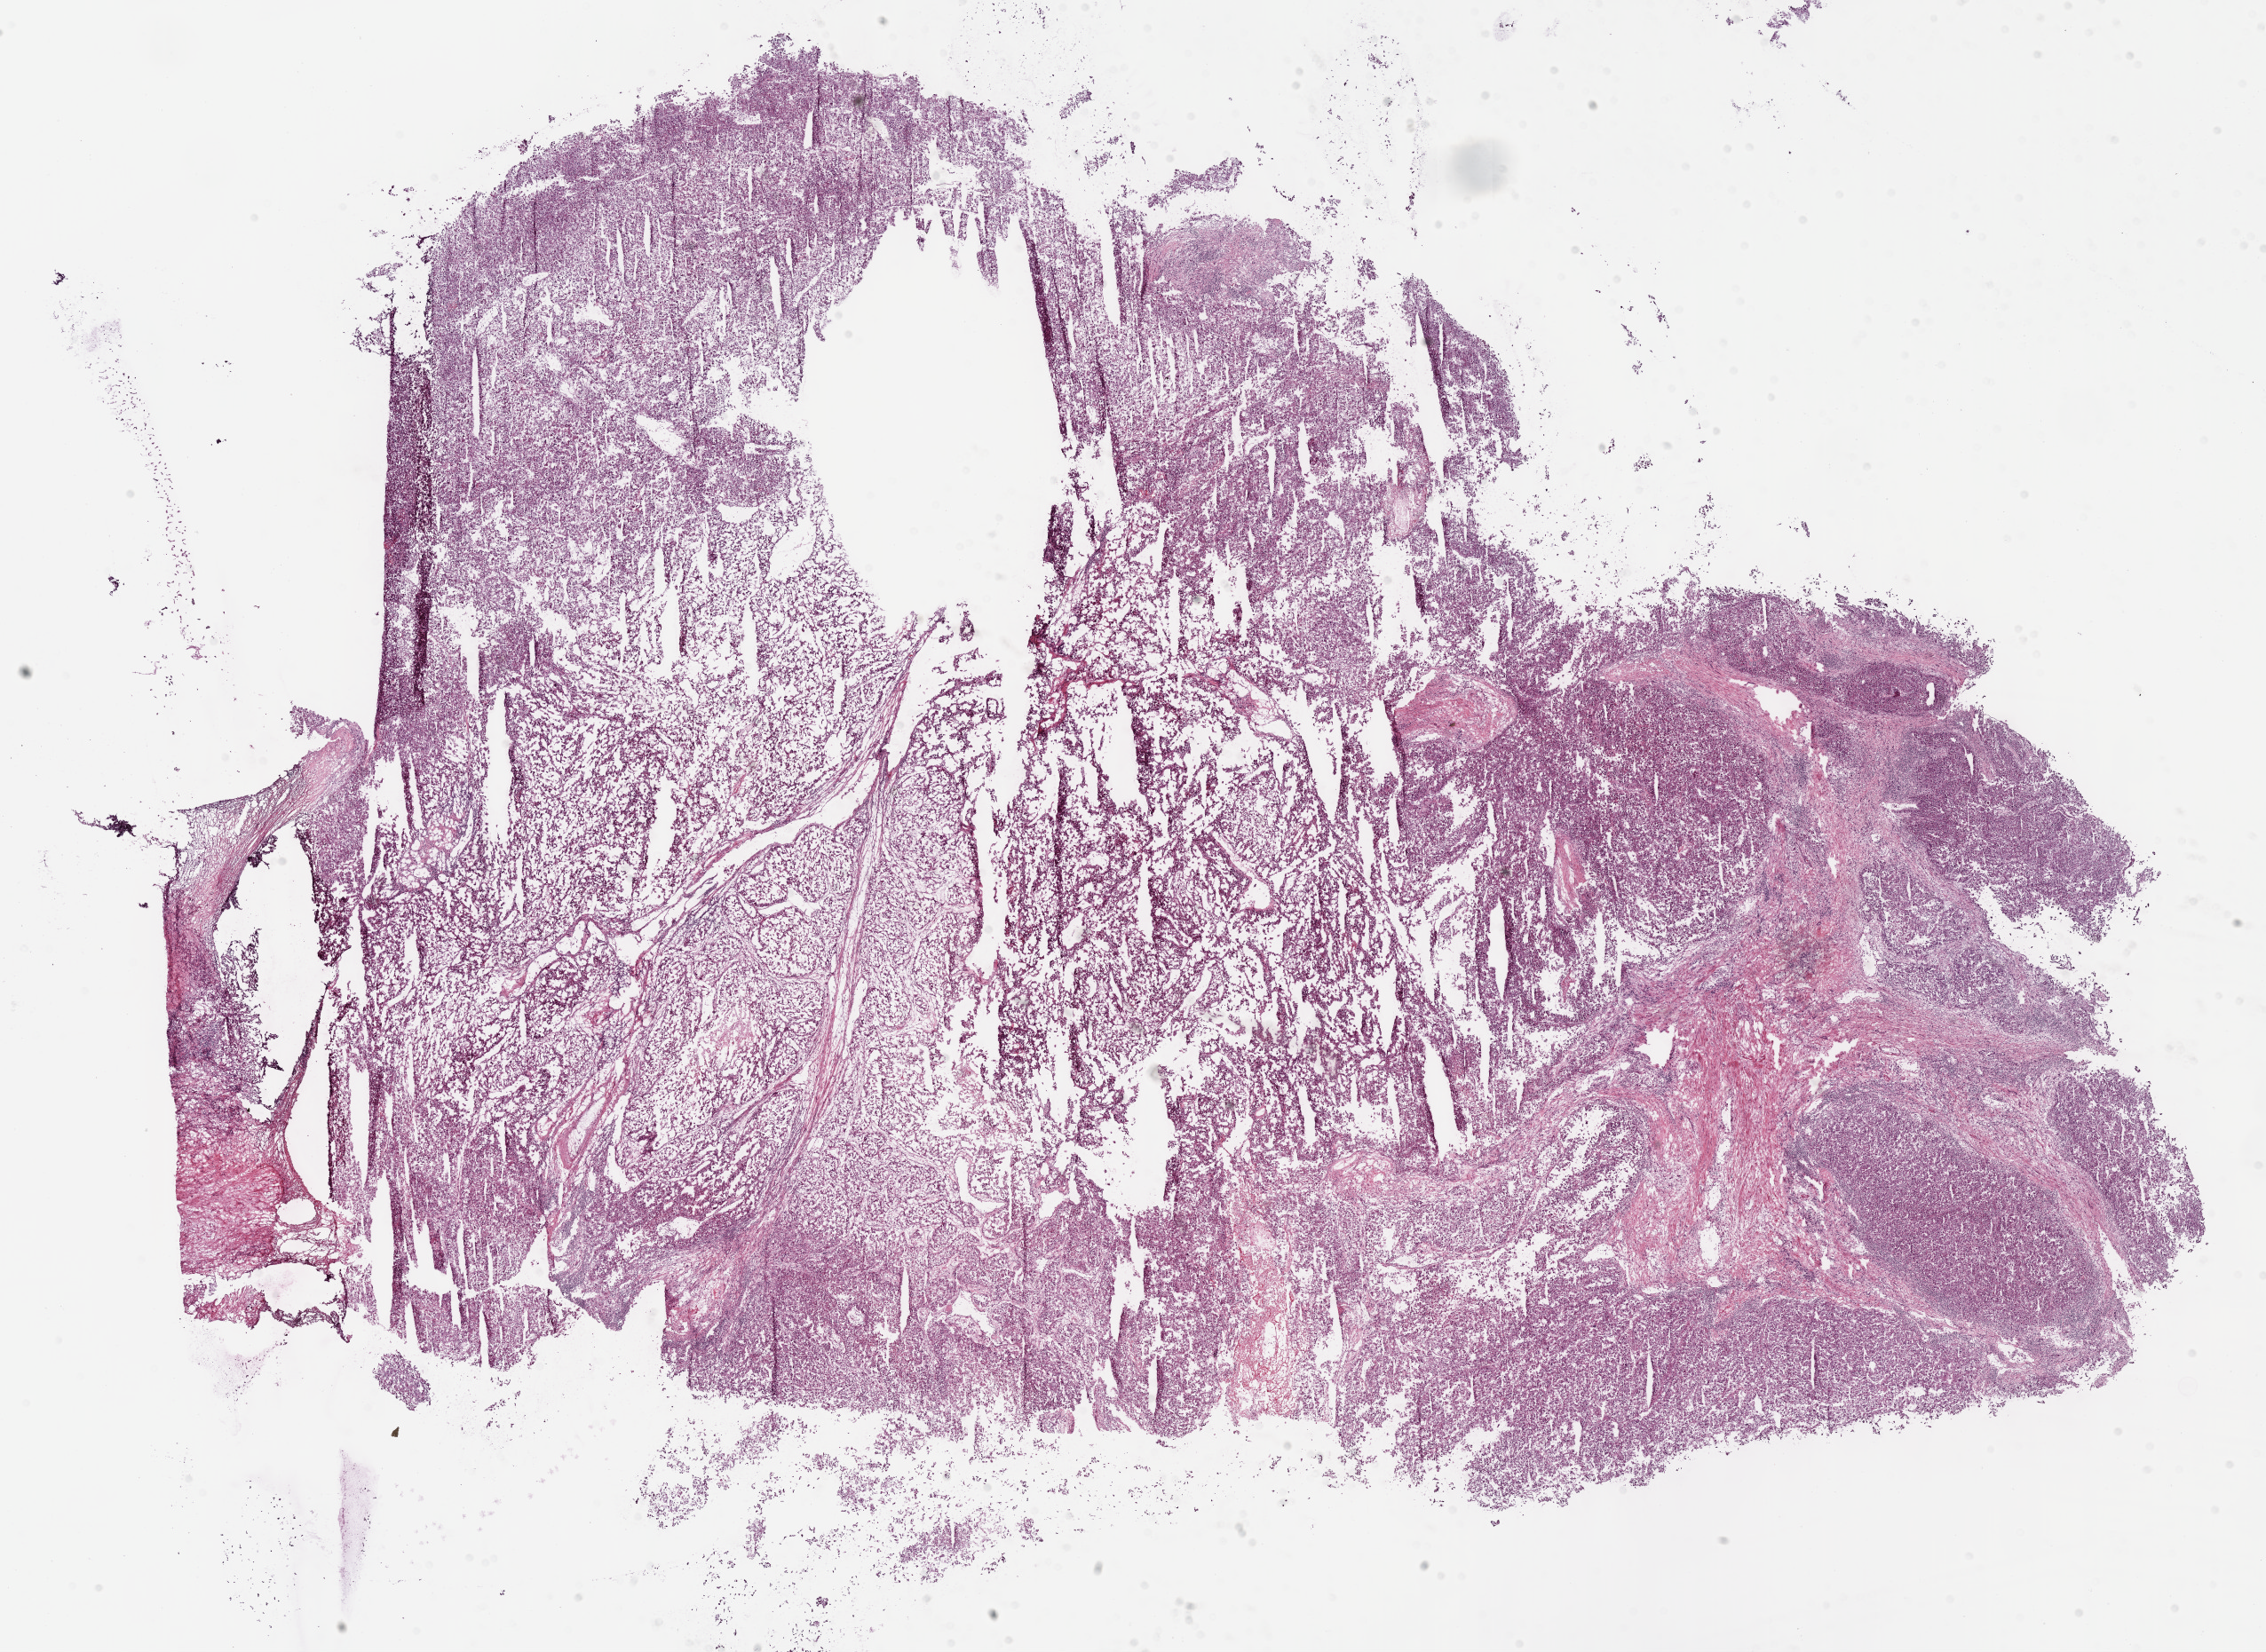
Whole-slide histology image, H&E-stained — a low-resolution overview of the entire scanned area, about 20.6 x 15.1 mm (slide scanned at 40x), frozen section from the bottom of the tissue portion, sample: primary tumour, kidney. Male, age 63 years at initial diagnosis.
Diagnosis: Clear cell adenocarcinoma, NOS.